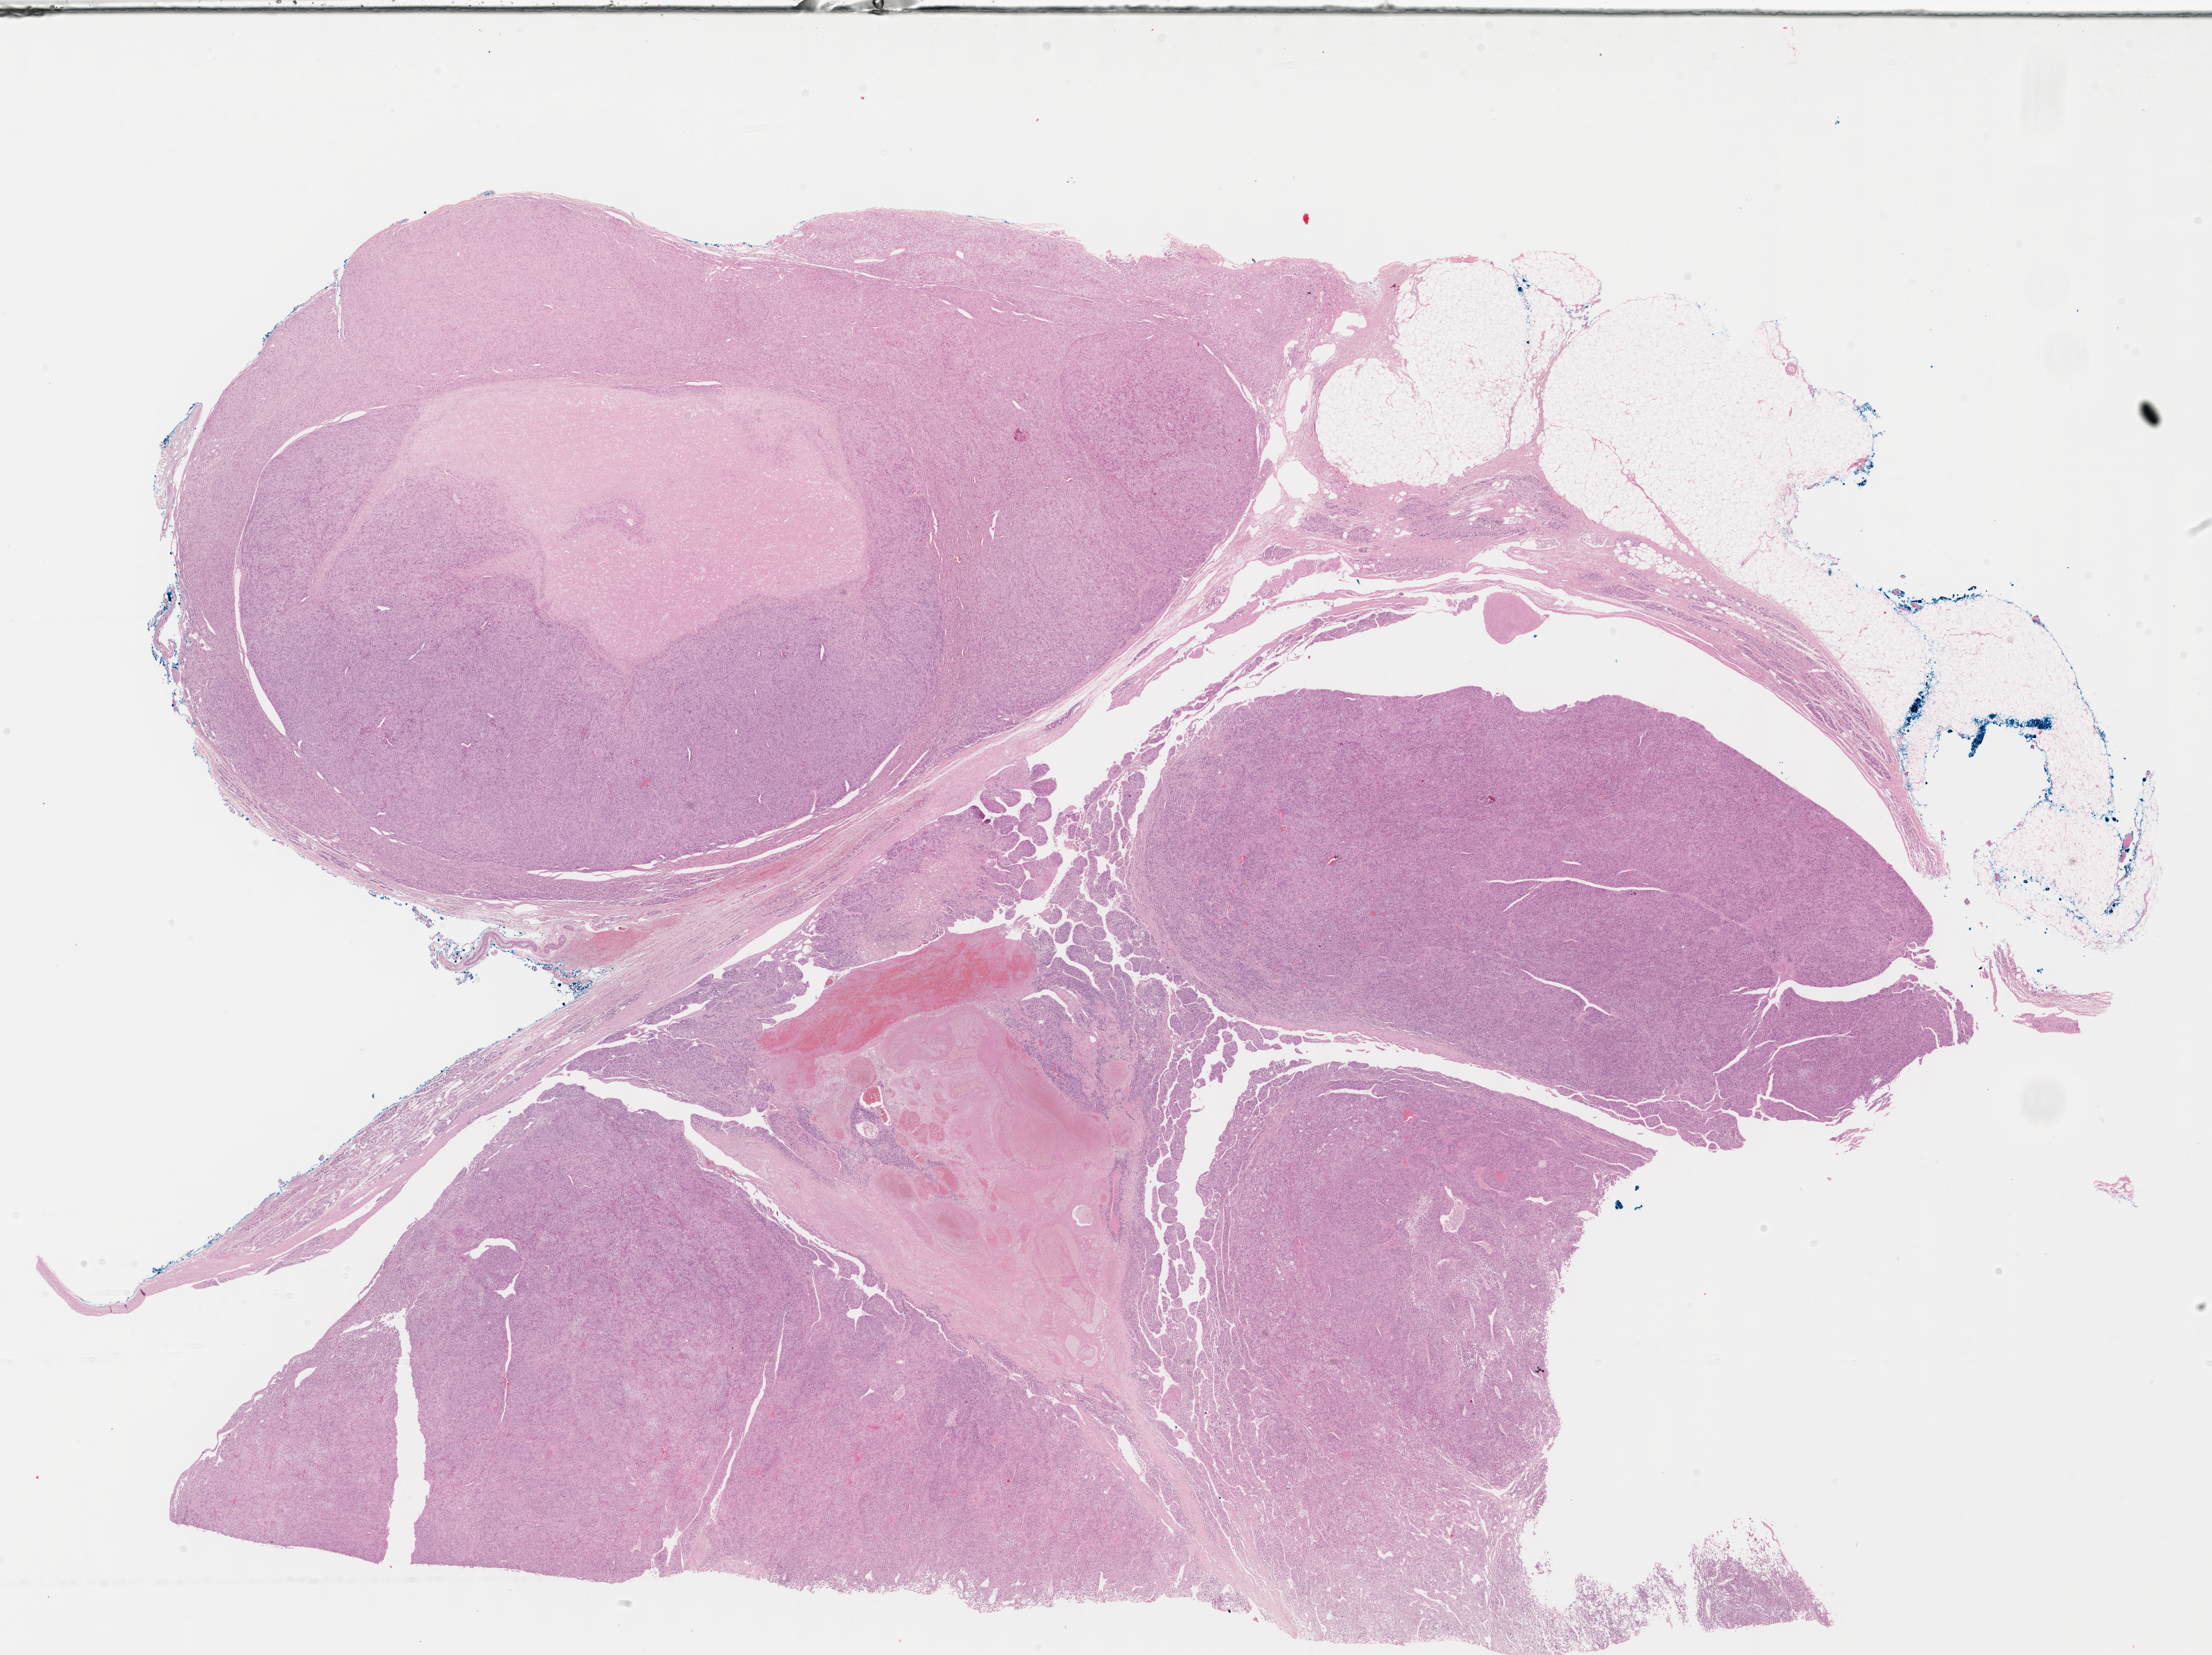
Digitized H&E tissue section (whole slide), shown as a low-resolution overview of the whole scanned area (about 25.7 x 19.2 mm, slide scanned at 40x), formalin-fixed paraffin-embedded (FFPE) diagnostic section, primary tumour sample from the adrenal cortex. Female patient; age at initial diagnosis 17 years.
Diagnosis: Adrenal cortical carcinoma (cortex of adrenal gland). Laterality: left.